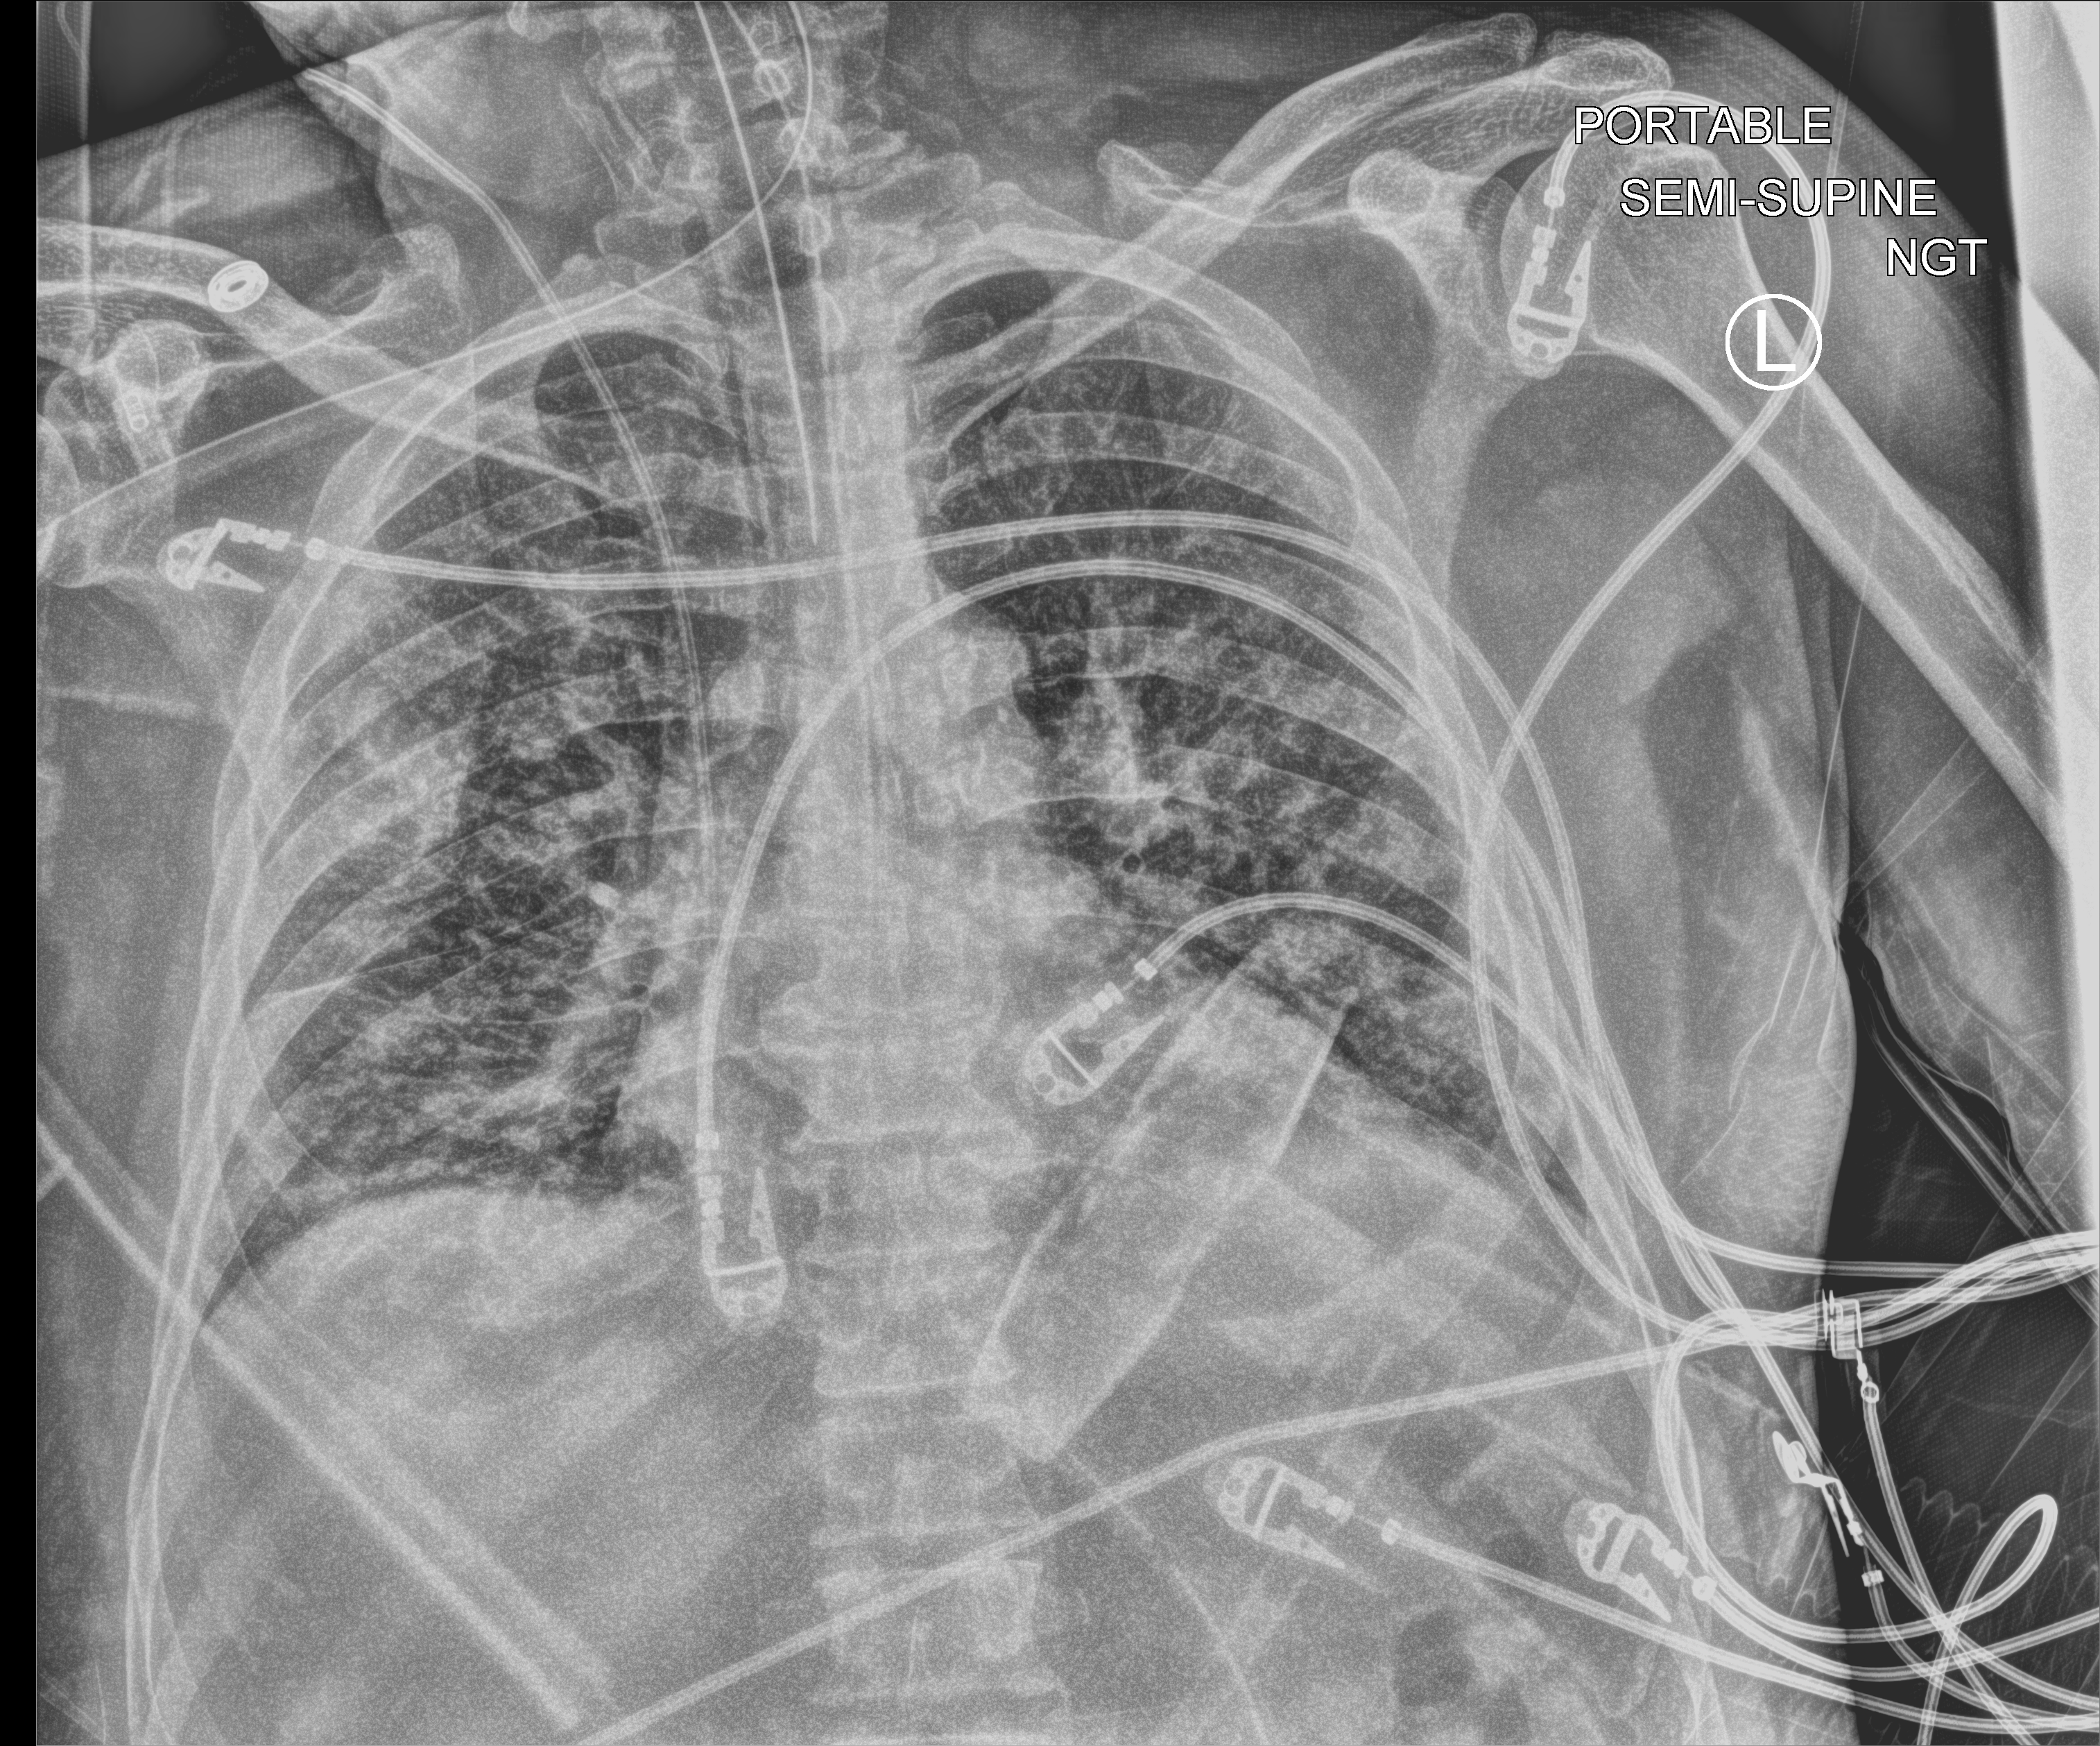
Chest X-ray (portable). Male patient hospitalised with COVID-19, age 18–59 years.
From the hospital-stay record, not from the radiograph (when in the stay this image was taken is not recorded): chronic kidney disease (admission record): no; length of hospital stay: 11 days; admitted to intensive care during this hospital stay: yes.